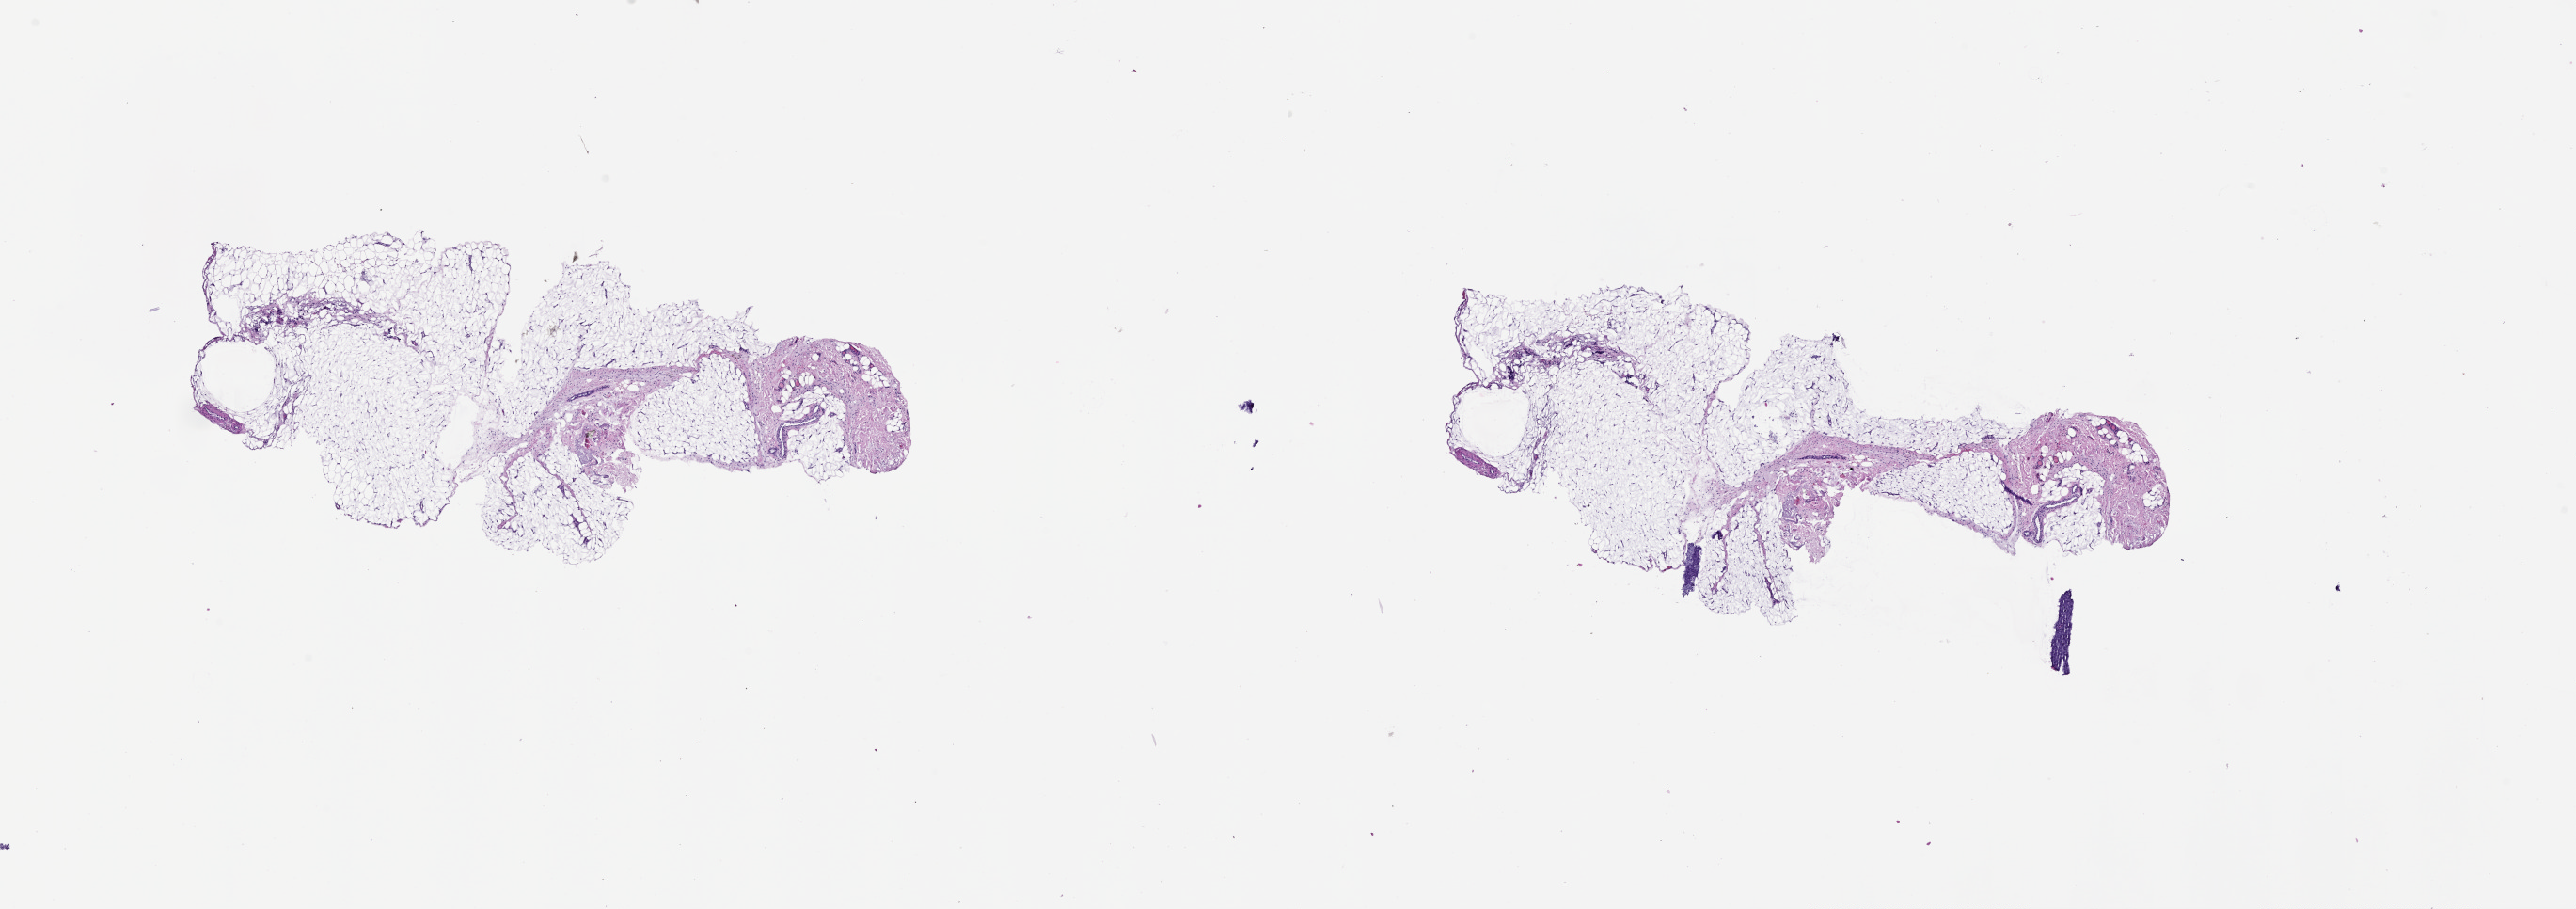
Whole-slide histology image, Hematoxylin and eosin (H&E) stained — whole scanned area (about 22.0 x 7.8 mm, acquisition: 20x scan) shown as a low-resolution overview. Normal (non-tumour) tissue sample, sampled site: lymph node. 53-year-old male patient.
* this section: normal (non-tumour) tissue from the same patient
* patient diagnosis: Malignant melanoma, NOS